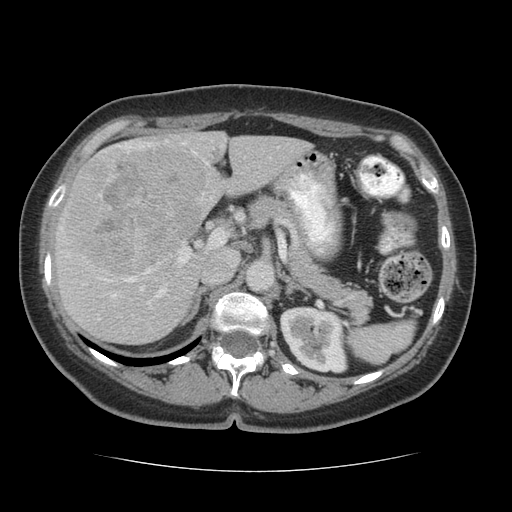
Contrast-enhanced abdominal CT (liver protocol), one axial slice. Slice 36 of 75 in the series (ordered by position). Soft-tissue window (W 400 / L 40 HU). 2.5 mm slice thickness. 512 × 512 image matrix. From the clinical record (not read from this slice): diagnosis: hepatocellular carcinoma (patient treated with transarterial chemoembolisation; whether this scan precedes or follows treatment is not stated here); TNM stage (as recorded): Stage-I; Child-Pugh class: A; tumour differentiation: moderately differentiated.
Annotated regions visible in this slice (semi-automatic segmentation, software-assisted and operator-edited):
- liver parenchyma outside the tumour (the mass and vessels are separate outlines, so this box may not span the whole liver): bounding box (x1, y1, x2, y2) in pixels: (54, 130, 310, 344)
- mass: (64, 144, 204, 277)
- liver vessels: (59, 142, 208, 304)